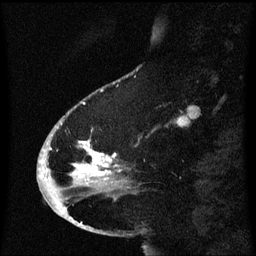
Breast MRI (dynamic contrast-enhanced), one sagittal slice; position 20 of 60 along the scan axis; dynamic contrast-enhanced series, image 2 of 3 at this slice position (ordered by acquisition); 1.5 T; TE 4.2 ms, TR 8.4 ms; 2.1 mm slice thickness; 256 × 256 image matrix, field of view 200 × 200 mm. Female patient, age 53 years. From the clinical record (not read from this slice): setting: breast cancer imaged before/during neoadjuvant chemotherapy; receptor status: HR-positive, HER2-negative.
Annotated regions visible in this slice (semi-automatically segmented with operator editing):
- analysis volume of interest (the breast-tissue region the enhancement analysis was run in; not a lesion): box from (x=49, y=112) to (x=130, y=201) px
- tumour enhancement mask (voxels above the 70 % enhancement threshold inside the analysis volume of interest): (x=73, y=140)–(x=113, y=177)